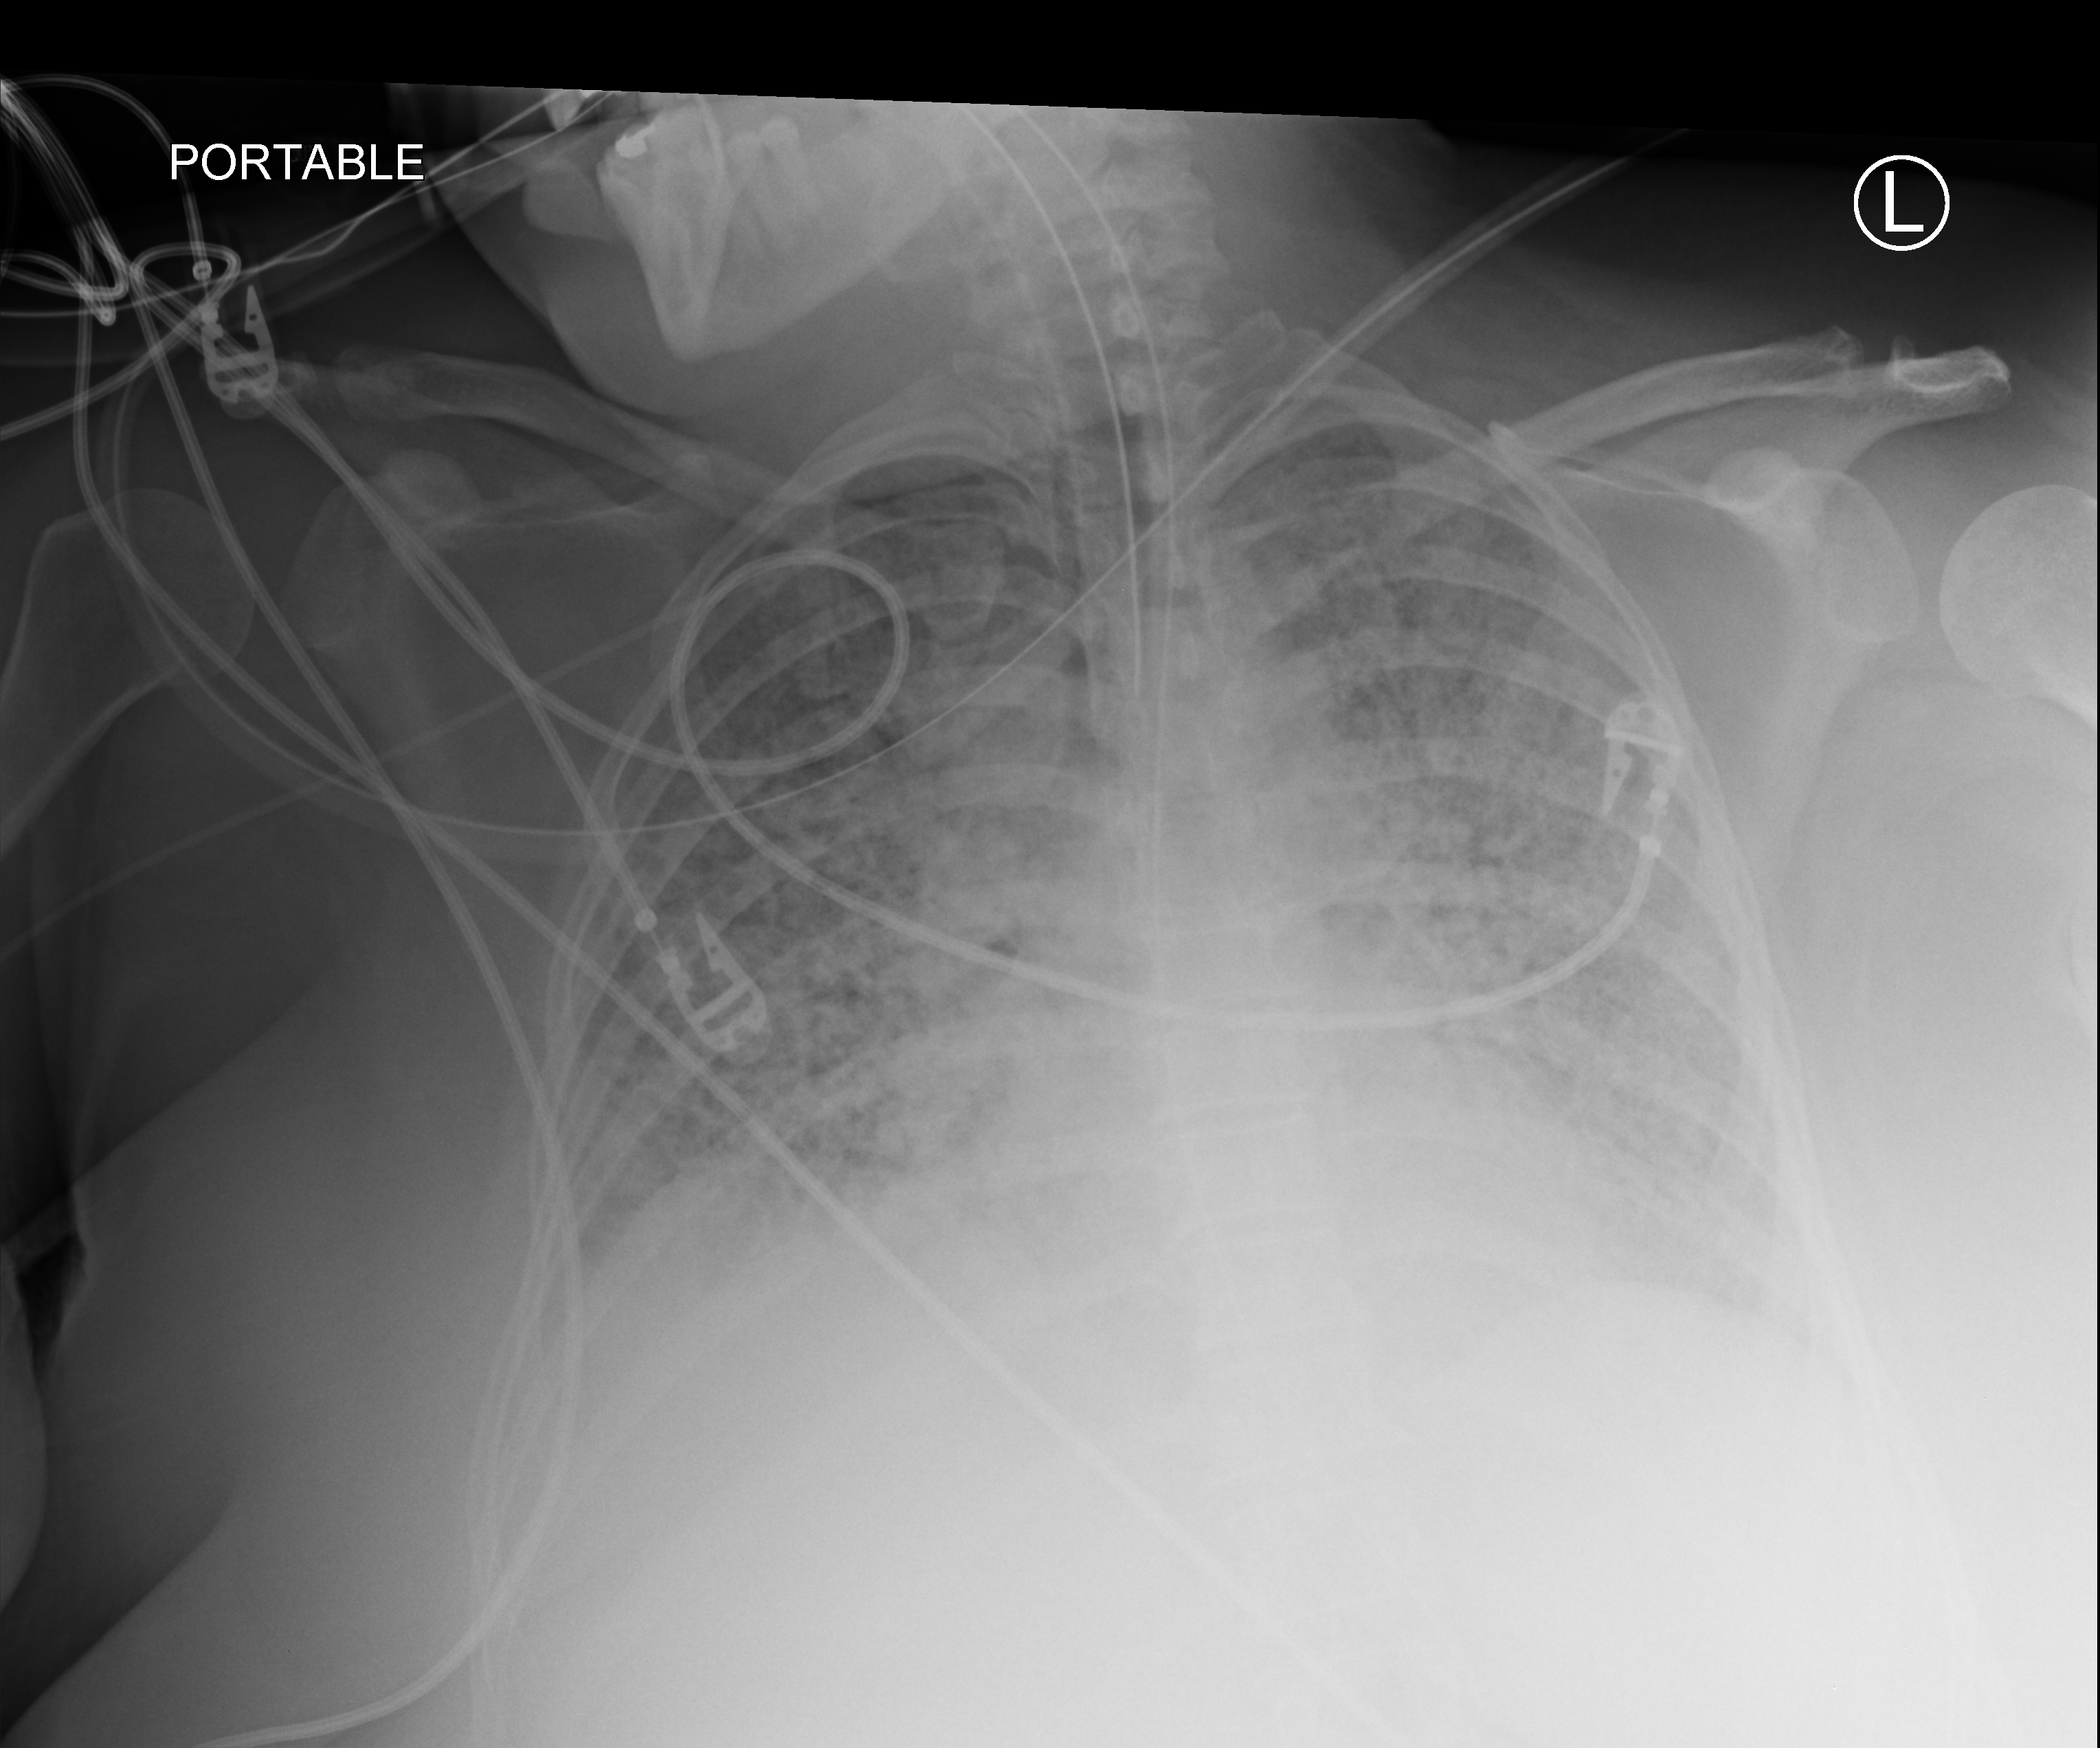
Portable chest radiograph; anteroposterior (AP) projection. Patient hospitalised with COVID-19; female, aged 18–59 years.
Admission-level facts for this patient (not findings on this image; timing relative to this image not recorded):
- mechanically ventilated during this hospital stay: yes